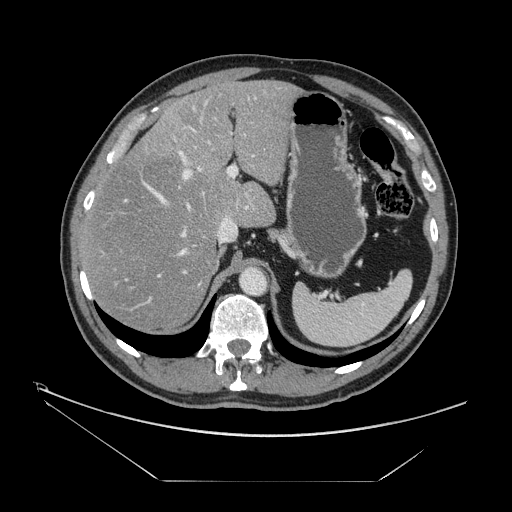
Contrast-enhanced abdominal CT, one axial slice; slice 103 of 161 in the series (ordered by position); intravenous contrast given; soft-tissue window (W 400 / L 40 HU); 512 × 512 image matrix, field of view 440 × 440 mm. Male patient, age 65 years. Case-level facts recorded for this patient, not image findings: diagnosis: colorectal cancer liver metastases, imaged before liver resection; multiple liver metastases: yes; largest metastasis: 4.2 cm; chemotherapy before resection: yes.
Structures marked on this image (manually delineated by an expert):
- hepatic veins: bounding box [x1, y1, x2, y2] px = [125, 128, 195, 281]
- liver: [82, 81, 296, 329]
- planned liver remnant (the part of the liver to remain after resection): [81, 81, 297, 329]
- portal vein (with intrahepatic branches): [112, 96, 257, 311]